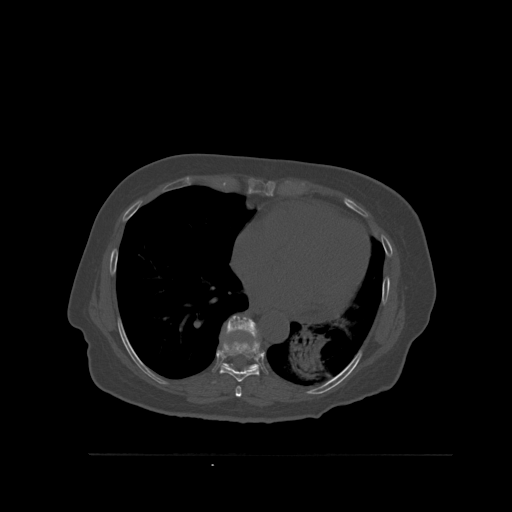
CT including the spine, one axial slice; position 347 of 527 along the scan axis; bone window (W 1800 / L 400 HU); 1.5 mm slice thickness; 512 × 512 image matrix, field of view 470 × 470 mm. Patient: female, 73 years. From the clinical record (not read from this slice): primary cancer: breast; vertebrae with lytic lesions (as recorded): L2.
Structures marked on this image (semi-automatic segmentation, software-assisted and operator-edited):
- T7 vertebra: bounding box (x1, y1, x2, y2) in pixels: (235, 386, 242, 397)
- T8 vertebra: (220, 343, 260, 382)
- T9 vertebra: (220, 316, 261, 371)